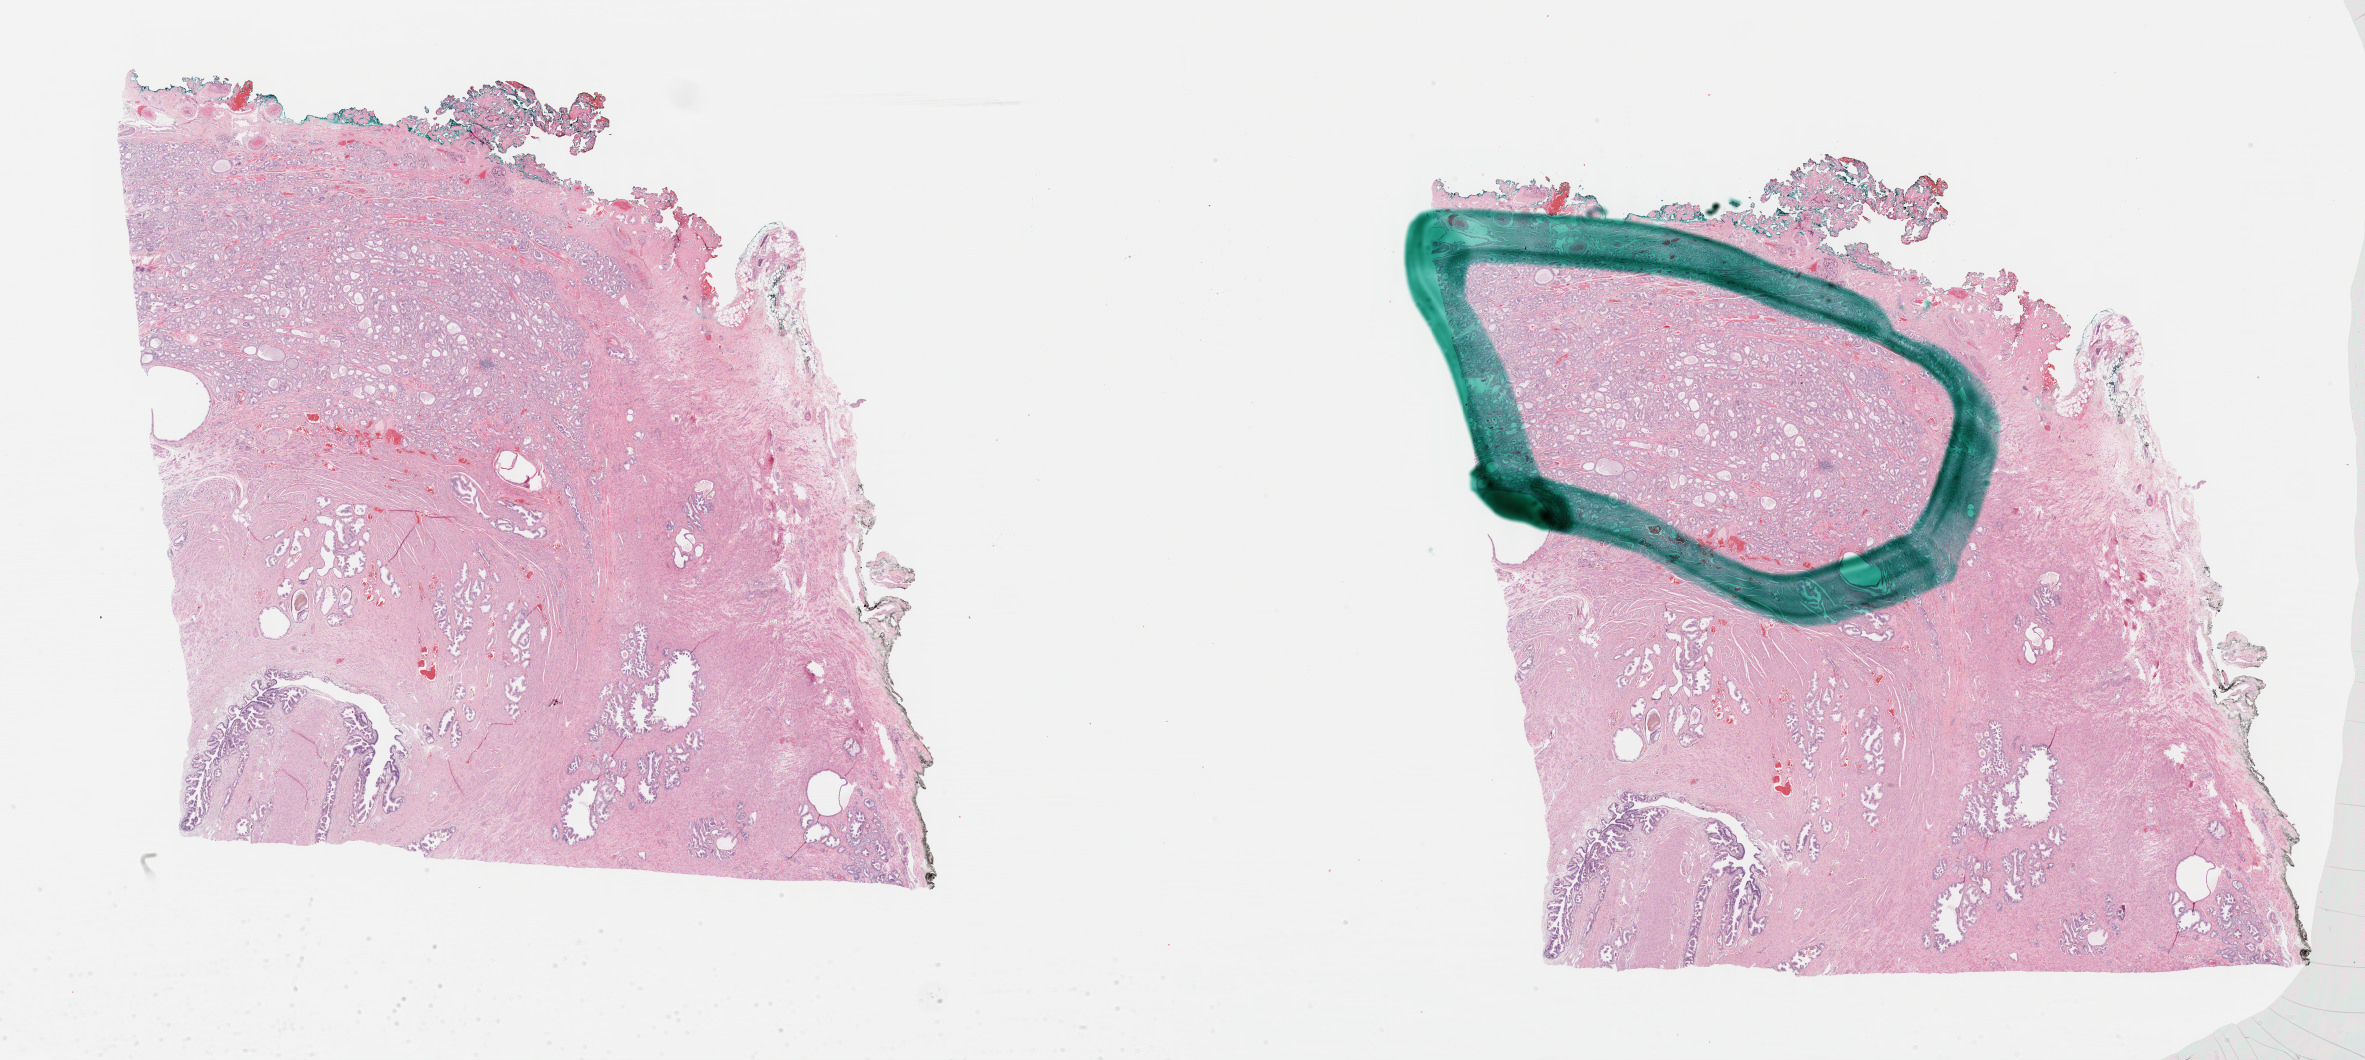
Whole-slide histology image, H&E-stained — a low-resolution overview of the entire scanned area, about 38.3 x 17.1 mm, formalin-fixed paraffin-embedded (FFPE) diagnostic section, primary tumour sample from the prostate. Male patient; age at initial diagnosis 49 years. Gleason score: 6 (3+3).
Diagnosis: Adenocarcinoma, NOS (prostate gland).